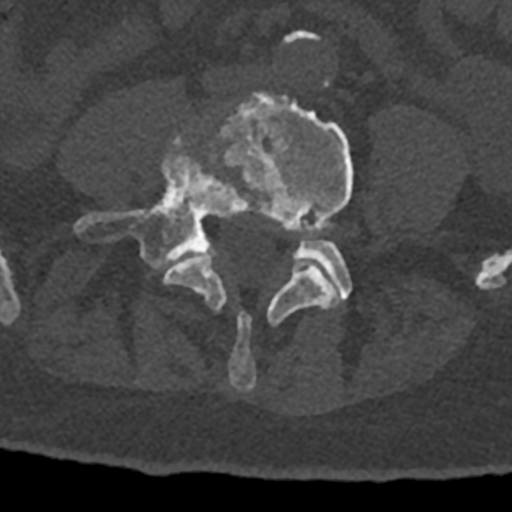
CT including the spine, one axial slice. Slice 231 of 797 in the series (ordered by position). Reconstruction kernel Br40s/3. Bone window (W 1800 / L 400 HU). 0.5 mm slice thickness. 512 × 512 image matrix, field of view 160 × 160 mm. Male patient, age 74 years. Case-level facts recorded for this patient, not image findings: primary cancer: renal.
Structures marked on this image (semi-automatically segmented with operator editing):
- L4 vertebra: box from (x=163, y=92) to (x=354, y=390) px
- L5 vertebra: (x=74, y=135)–(x=352, y=300)